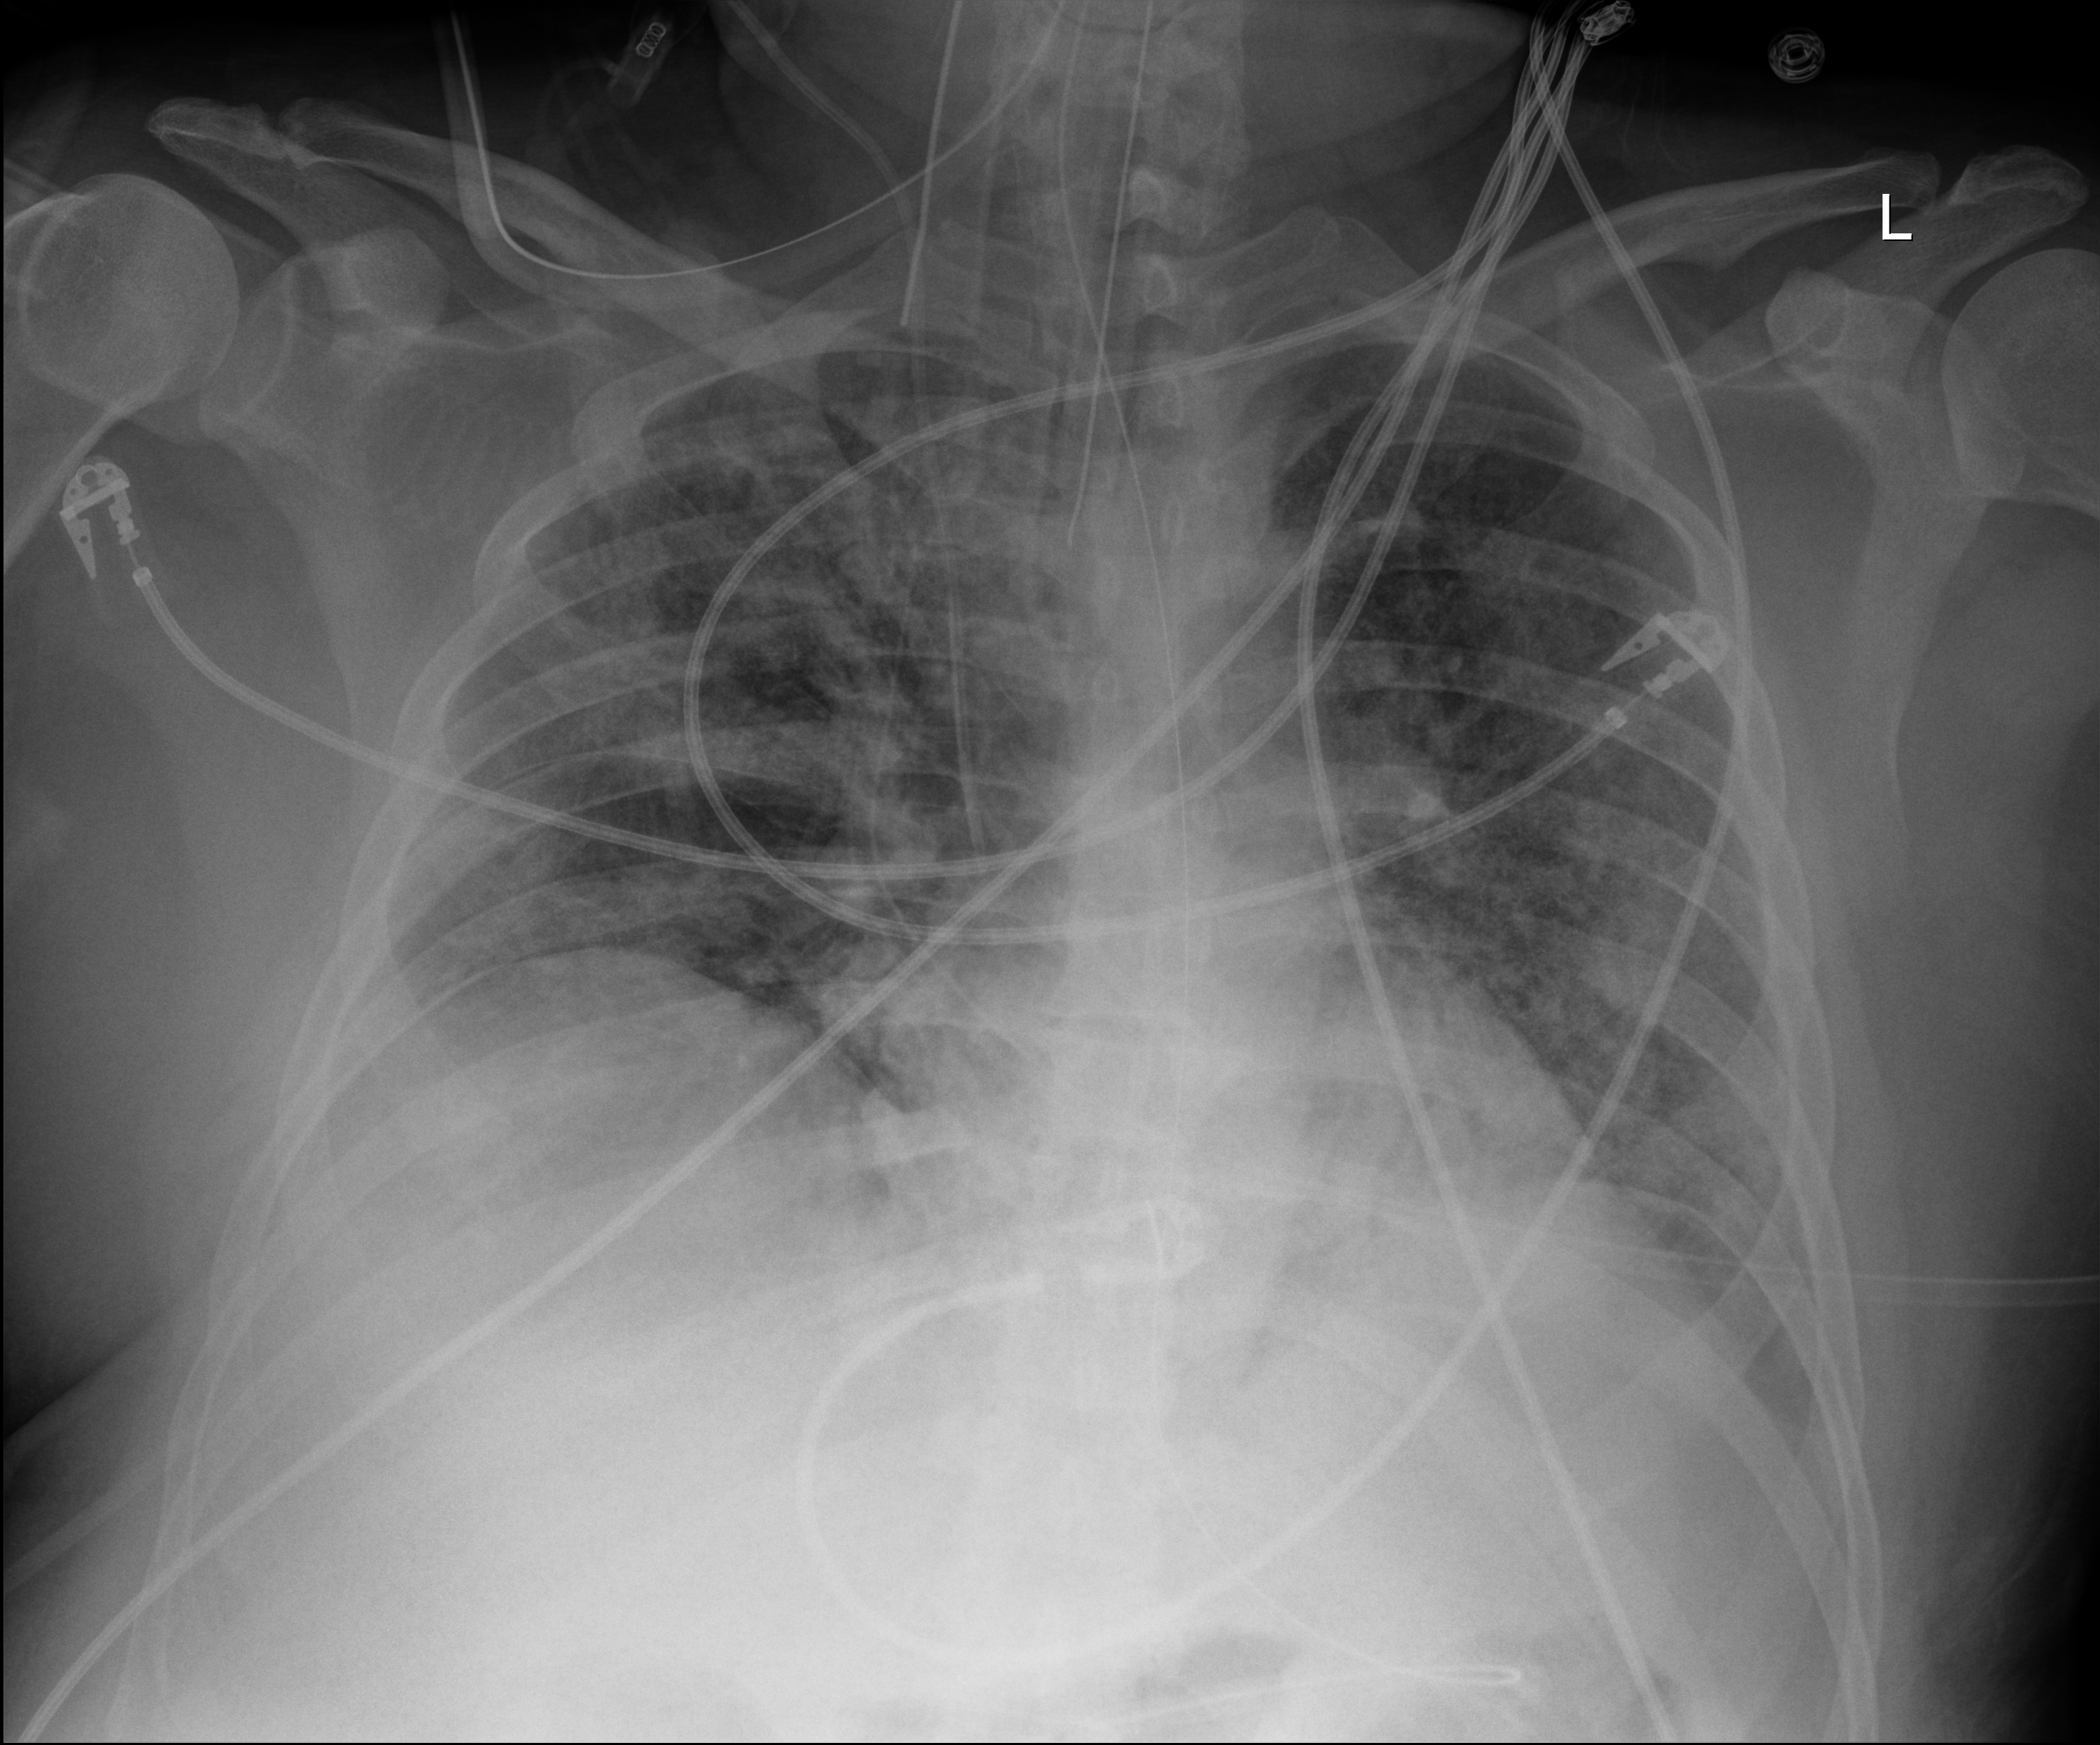
Chest X-ray (portable), anteroposterior (AP) projection. Male patient hospitalised with COVID-19, age 18–59 years.
Admission-level facts for this patient (not findings on this image; timing relative to this image not recorded): COPD (admission record): no; length of hospital stay: 96 days; admitted to intensive care during this hospital stay: yes.